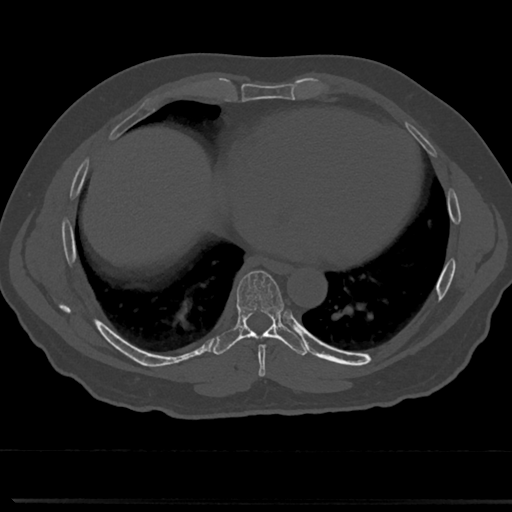
CT including the spine, one axial slice; slice 366 of 817 in the series (ordered by position); reconstruction kernel Br40s/3; bone window (W 1800 / L 400 HU); 0.5 mm slice thickness; 512 × 512 image matrix, field of view 355 × 355 mm. Patient: male, 61 years. Case-level facts recorded for this patient, not image findings: primary cancer: prostate.
Structures marked on this image (semi-automatic segmentation, software-assisted and operator-edited):
- T7 vertebra: bounding box (x1, y1, x2, y2) in pixels: (236, 272, 287, 359)
- T8 vertebra: (237, 322, 283, 335)